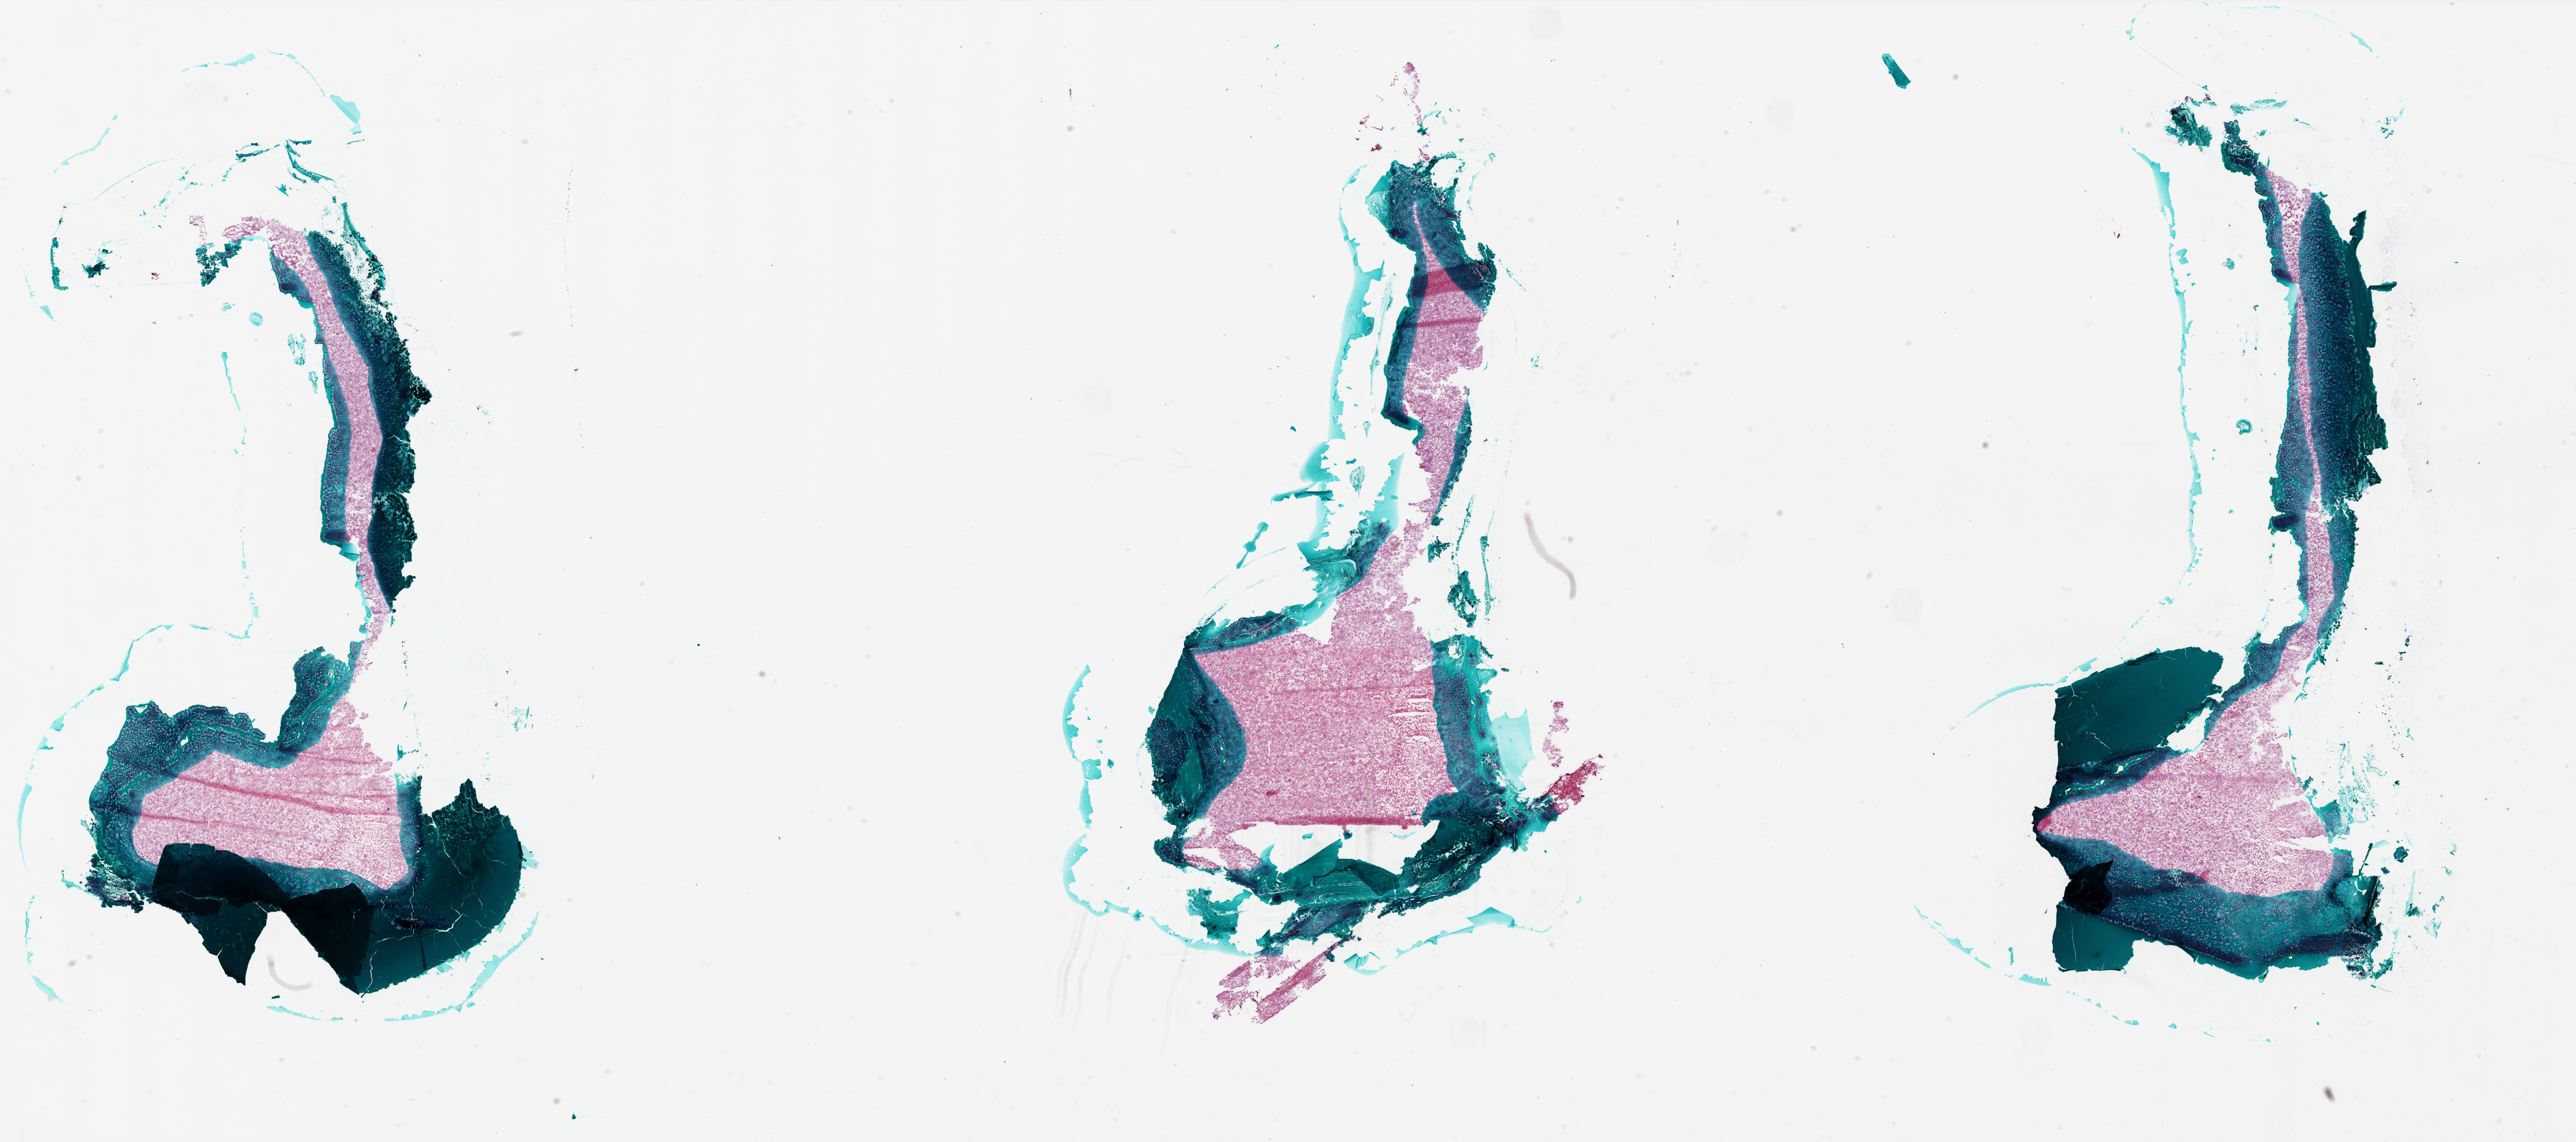
H&E whole-slide image, a low-resolution overview of the entire scanned area, about 40.0 x 17.7 mm (acquisition: 20x scan); frozen section from the bottom of the tissue portion; sample: primary tumour, brain. Male patient; age at initial diagnosis 54 years. Pathologist review of this section (percent, as recorded): tumour cells 90%, tumour nuclei 100%, normal cells 0%, stromal cells 0%, necrosis 10%.
* histologic diagnosis: Glioblastoma